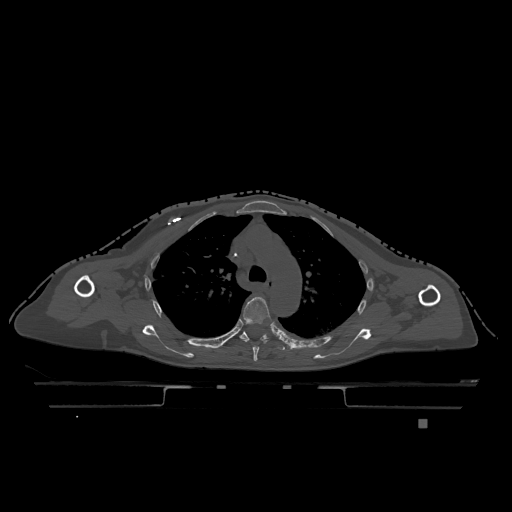
CT including the spine, one axial slice; slice 862 of 1317 in the series (ordered by position); bone window (W 1800 / L 400 HU); 0.5 mm slice thickness; 512 × 512 image matrix. Female patient, age 74 years. From the clinical record (not read from this slice): primary cancer: lung; vertebrae with lytic lesions (as recorded): T1, T4, T5, T6, L4, L5.
Structures marked on this image (semi-automatically segmented with operator editing):
- T4 vertebra: bounding box <240,297,272,361> (left, top, right, bottom; pixels)
- T5 vertebra: <221,331,285,350>